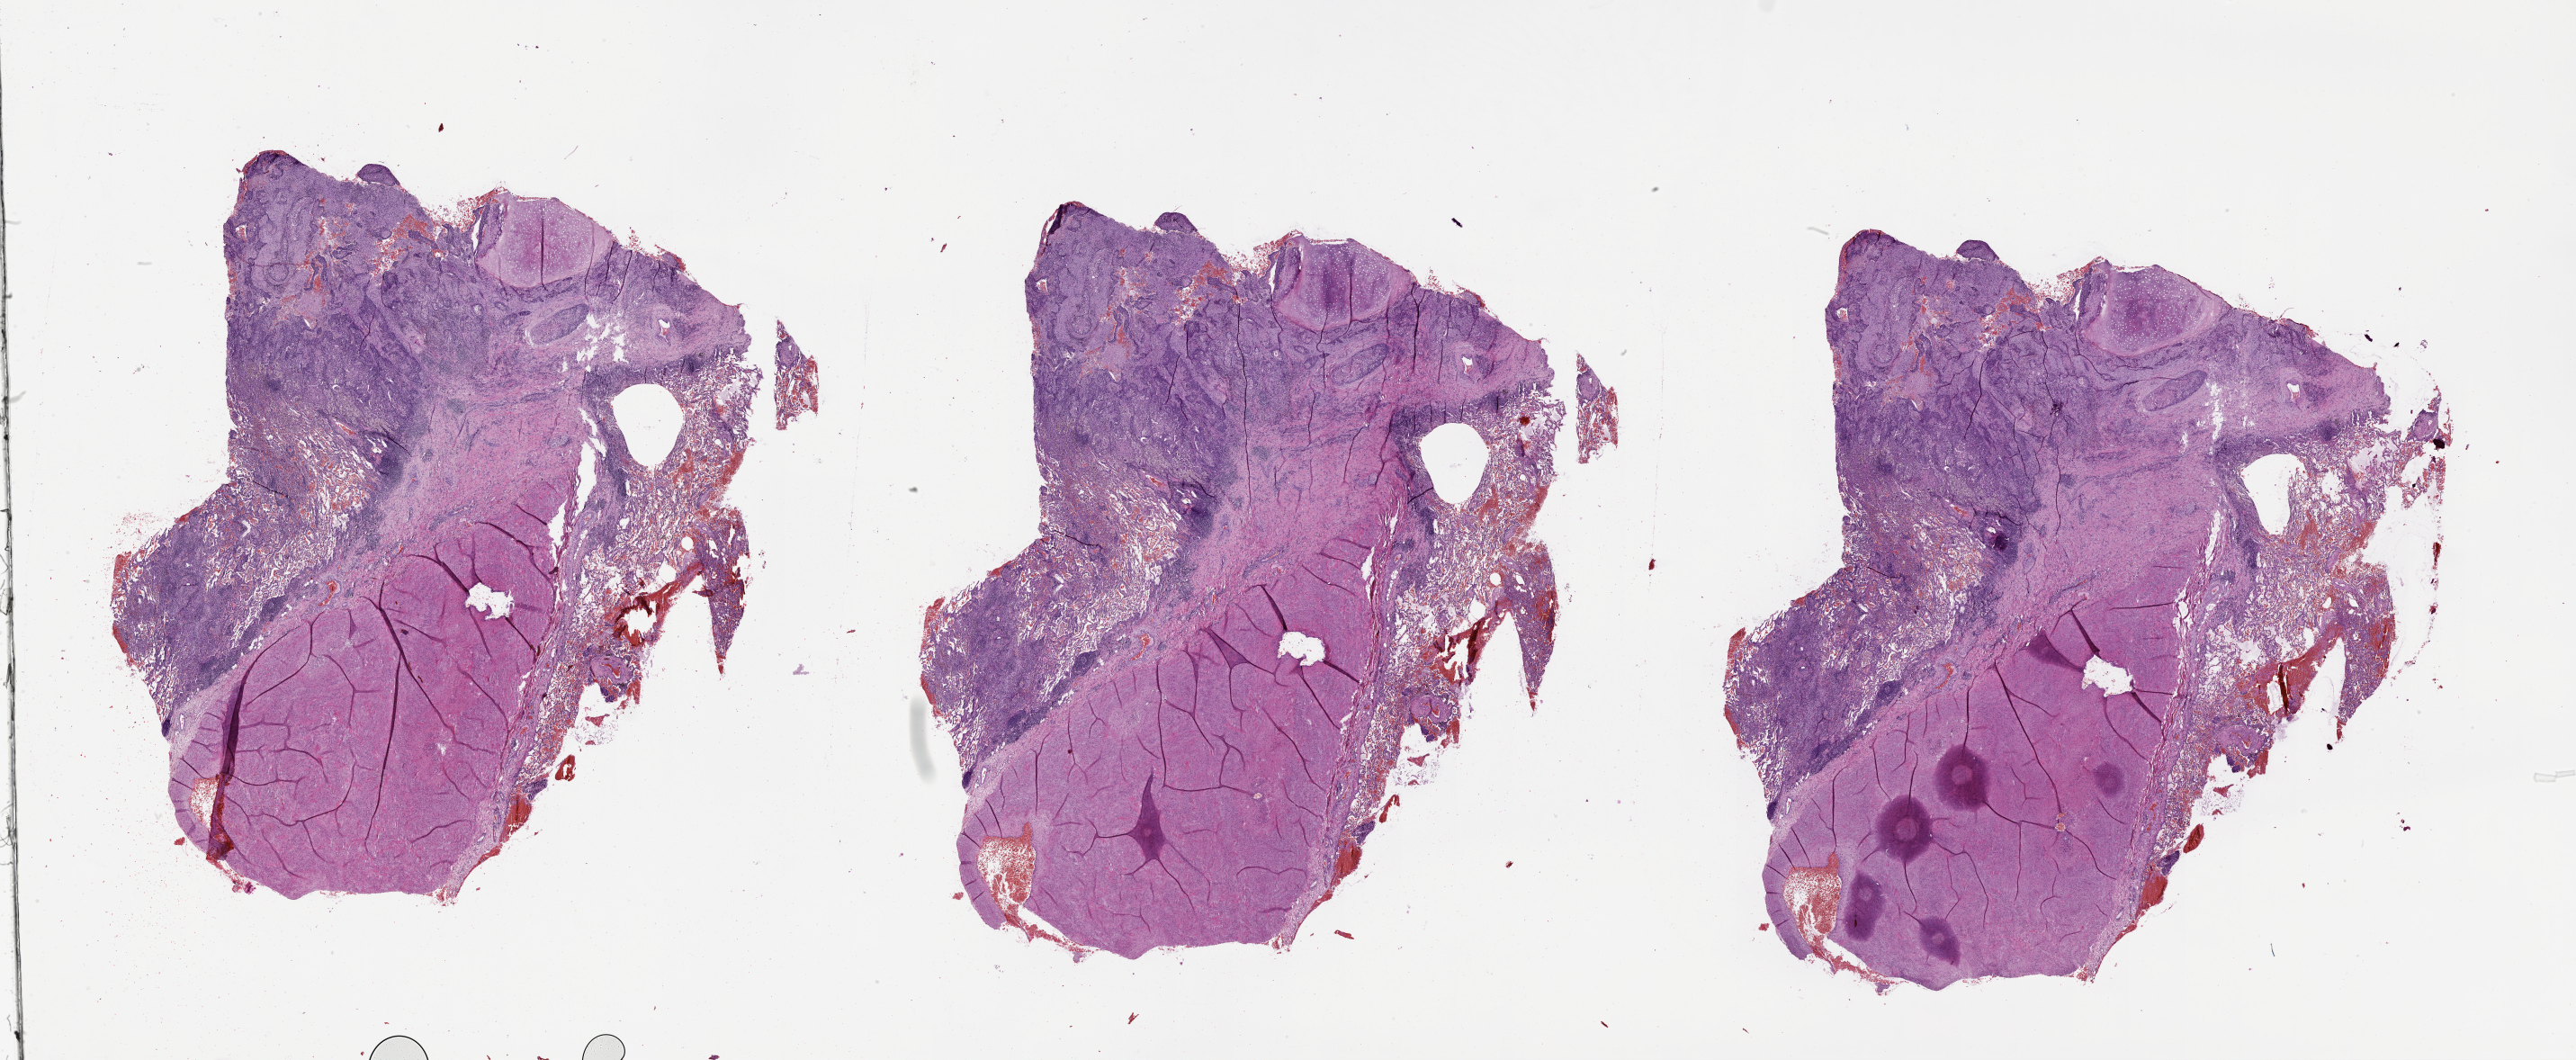
Digitized H&E-stained tissue section (whole slide), whole scanned area (about 46.1 x 19.0 mm, slide scanned at 20x) shown as a low-resolution overview; lung, tumour tissue. 49-year-old male patient.
Patient diagnosis (cohort enrolment): squamous cell carcinoma (lung).